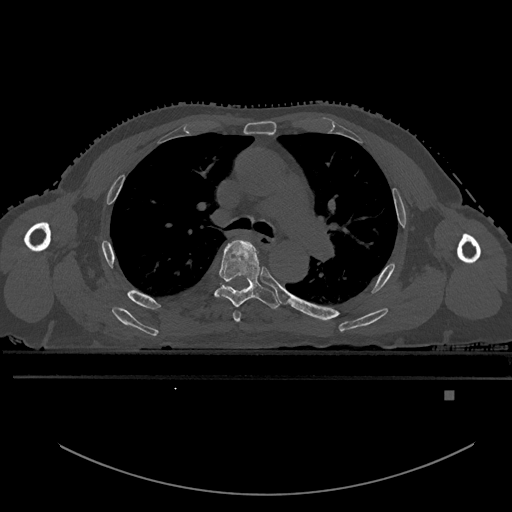
CT including the spine, one axial slice. Position 363 of 969 along the scan axis. Bone window (W 1800 / L 400 HU). 0.5 mm slice thickness. 512 × 512 image matrix. Patient: male, 82 years. Case-level facts recorded for this patient, not image findings: primary cancer: prostate; vertebrae with lytic lesions (as recorded): T11, T9, T8, T2.
Outlined on this slice (semi-automatically segmented with operator editing):
- T4 vertebra: box from (x=233, y=311) to (x=241, y=323) px
- T5 vertebra: (x=215, y=240)–(x=280, y=309)